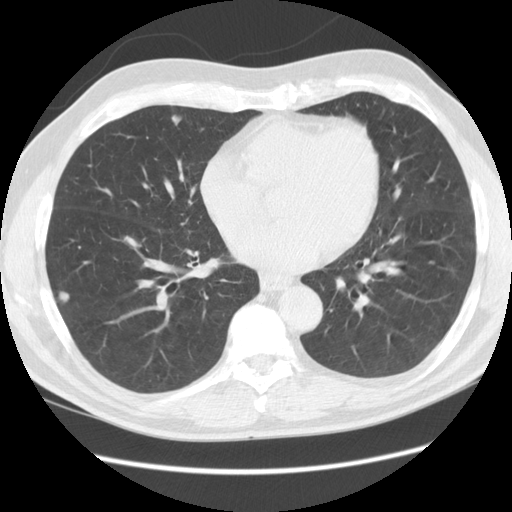
Low-dose screening chest CT, one axial slice; position 41 of 111 along the scan axis; lung window (W 1500 / L -600 HU); 512 × 512 image matrix, field of view 370 × 370 mm.
Structures marked on this image (outlined manually by an expert reader):
- lesion 2 (nodule, lower lobe of right lung): bounding box (x1, y1, x2, y2) in pixels: (59, 291, 69, 303)